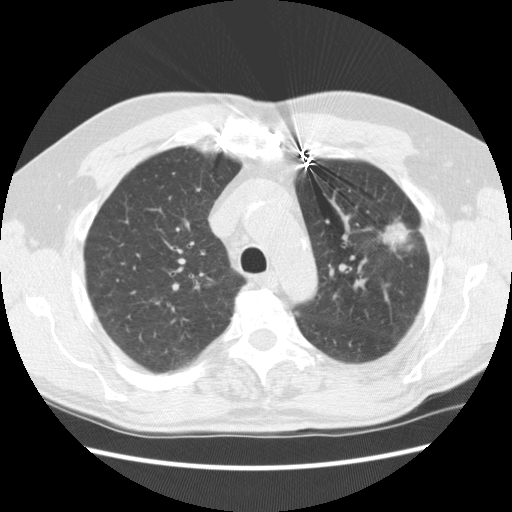
Low-dose screening chest CT, one axial slice; slice 177 of 231 in the series (ordered by position); reconstruction kernel STANDARD; 120 kVp; lung window (W 1500 / L -600 HU); 512 × 512 image matrix.
Annotated regions visible in this slice (outlined manually by an expert reader):
- lesion 1 (tumor, upper lobe of left lung): box from (x=382, y=222) to (x=410, y=244) px